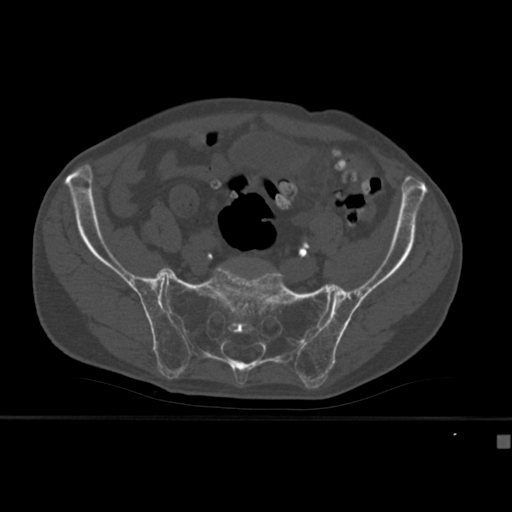
CT including the spine, one axial slice; position 64 of 430 along the scan axis; reconstruction kernel Br40s; 120 kVp; bone window (W 1800 / L 400 HU); 1.5 mm slice thickness; 512 × 512 image matrix, field of view 337 × 337 mm. Patient: male, 64 years. From the clinical record (not read from this slice): primary cancer: uterus; vertebrae with lytic lesions (as recorded): T1, T4, T5, T7, L5.
Outlined on this slice (semi-automatically segmented with operator editing):
- L5 vertebra: bounding box <242,261,272,269> (left, top, right, bottom; pixels)